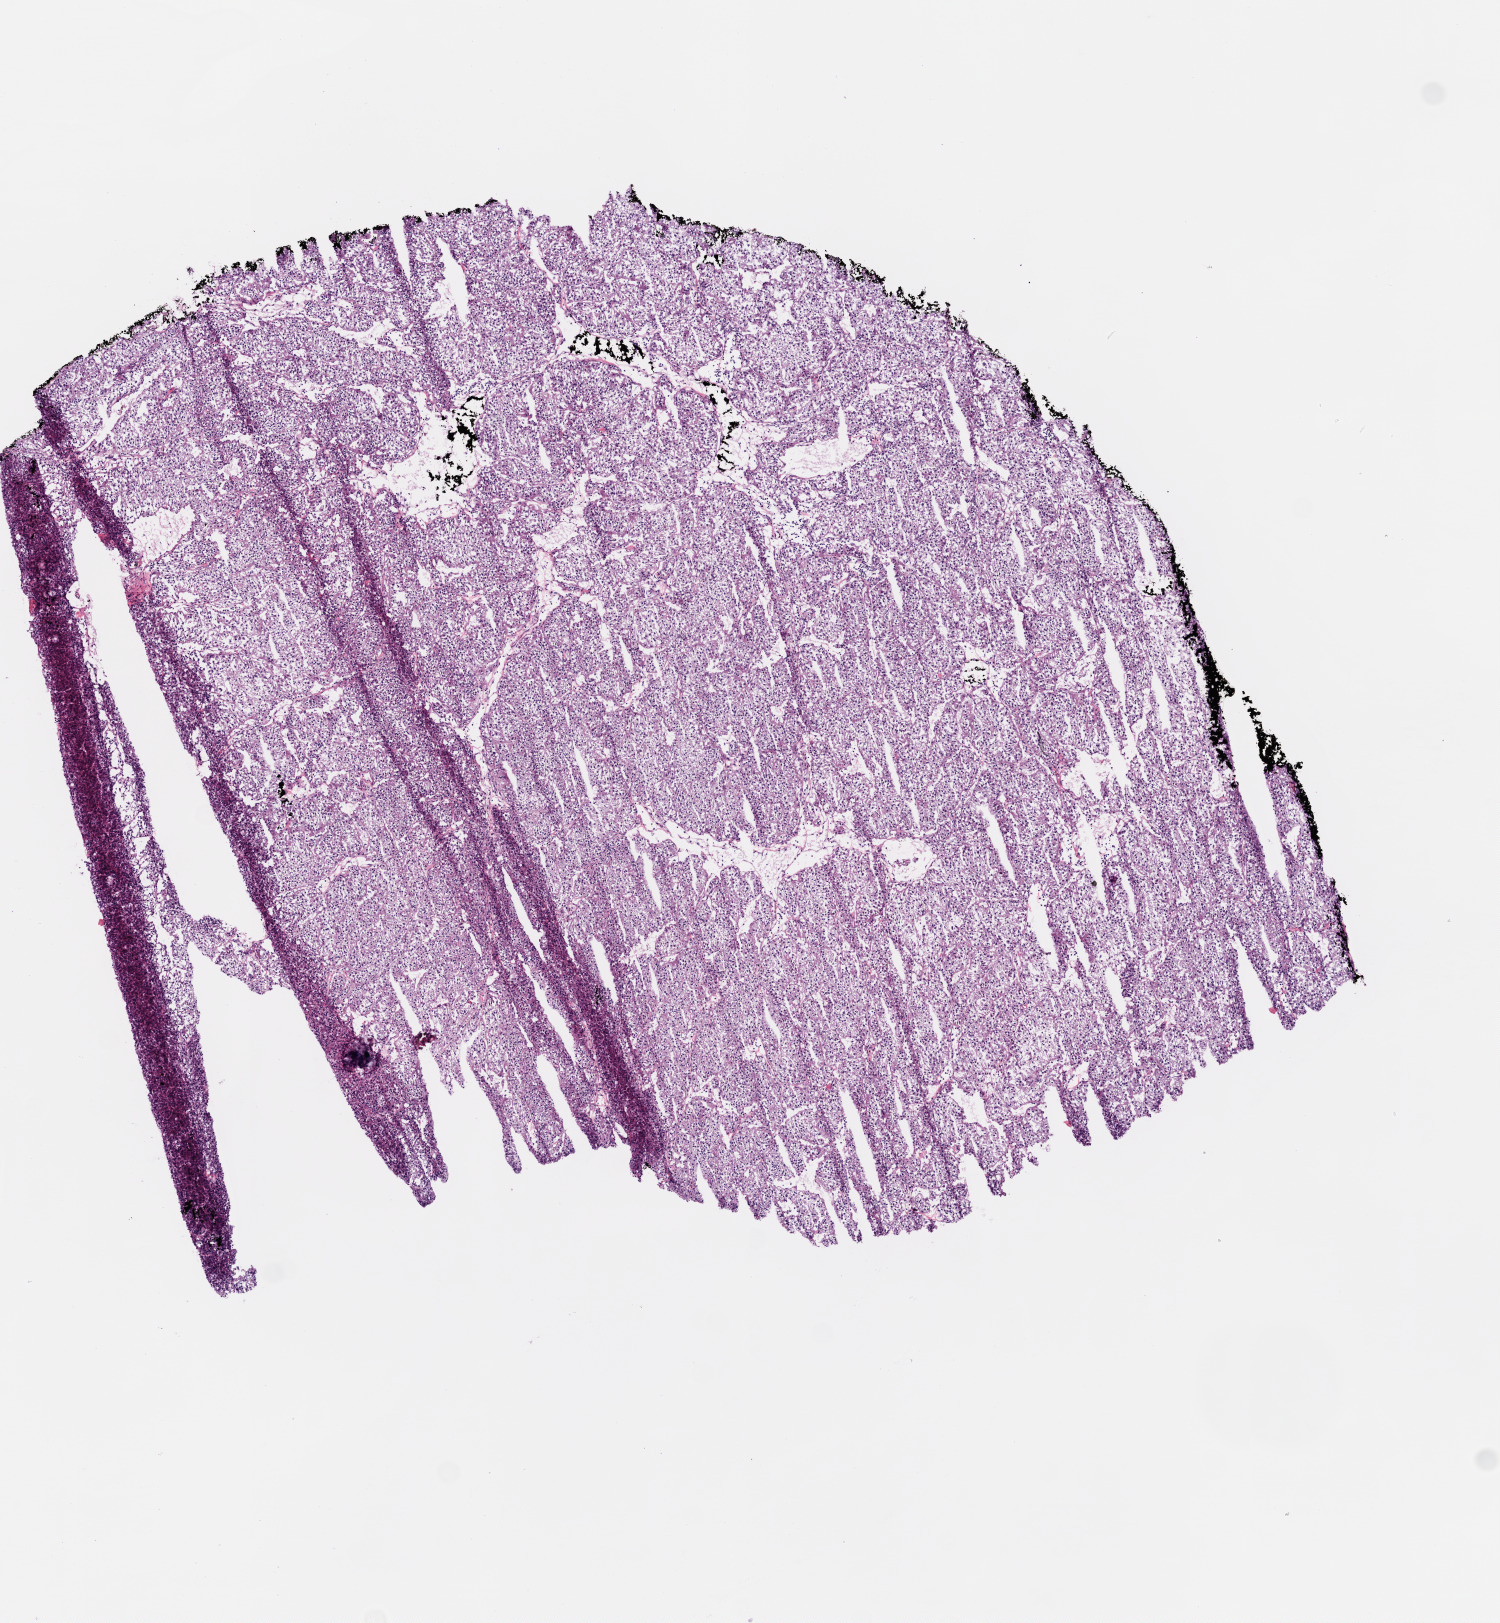
Hematoxylin and eosin (H&E) stained whole-slide image — a low-resolution overview of the entire scanned area, about 6.0 x 6.5 mm (from a 20x scan). Frozen section from the top of the tissue portion. Sample: primary tumour, kidney. Patient: male, age at initial diagnosis 67 years. Histologic grade: G3 (poorly differentiated). Pathologist review of this section (percent, as recorded): tumour cells 95%, tumour nuclei 90%, normal cells 0%, stromal cells 5%, necrosis 0%.
• AJCC pathologic stage: I
• pathologic diagnosis: Clear cell adenocarcinoma, NOS